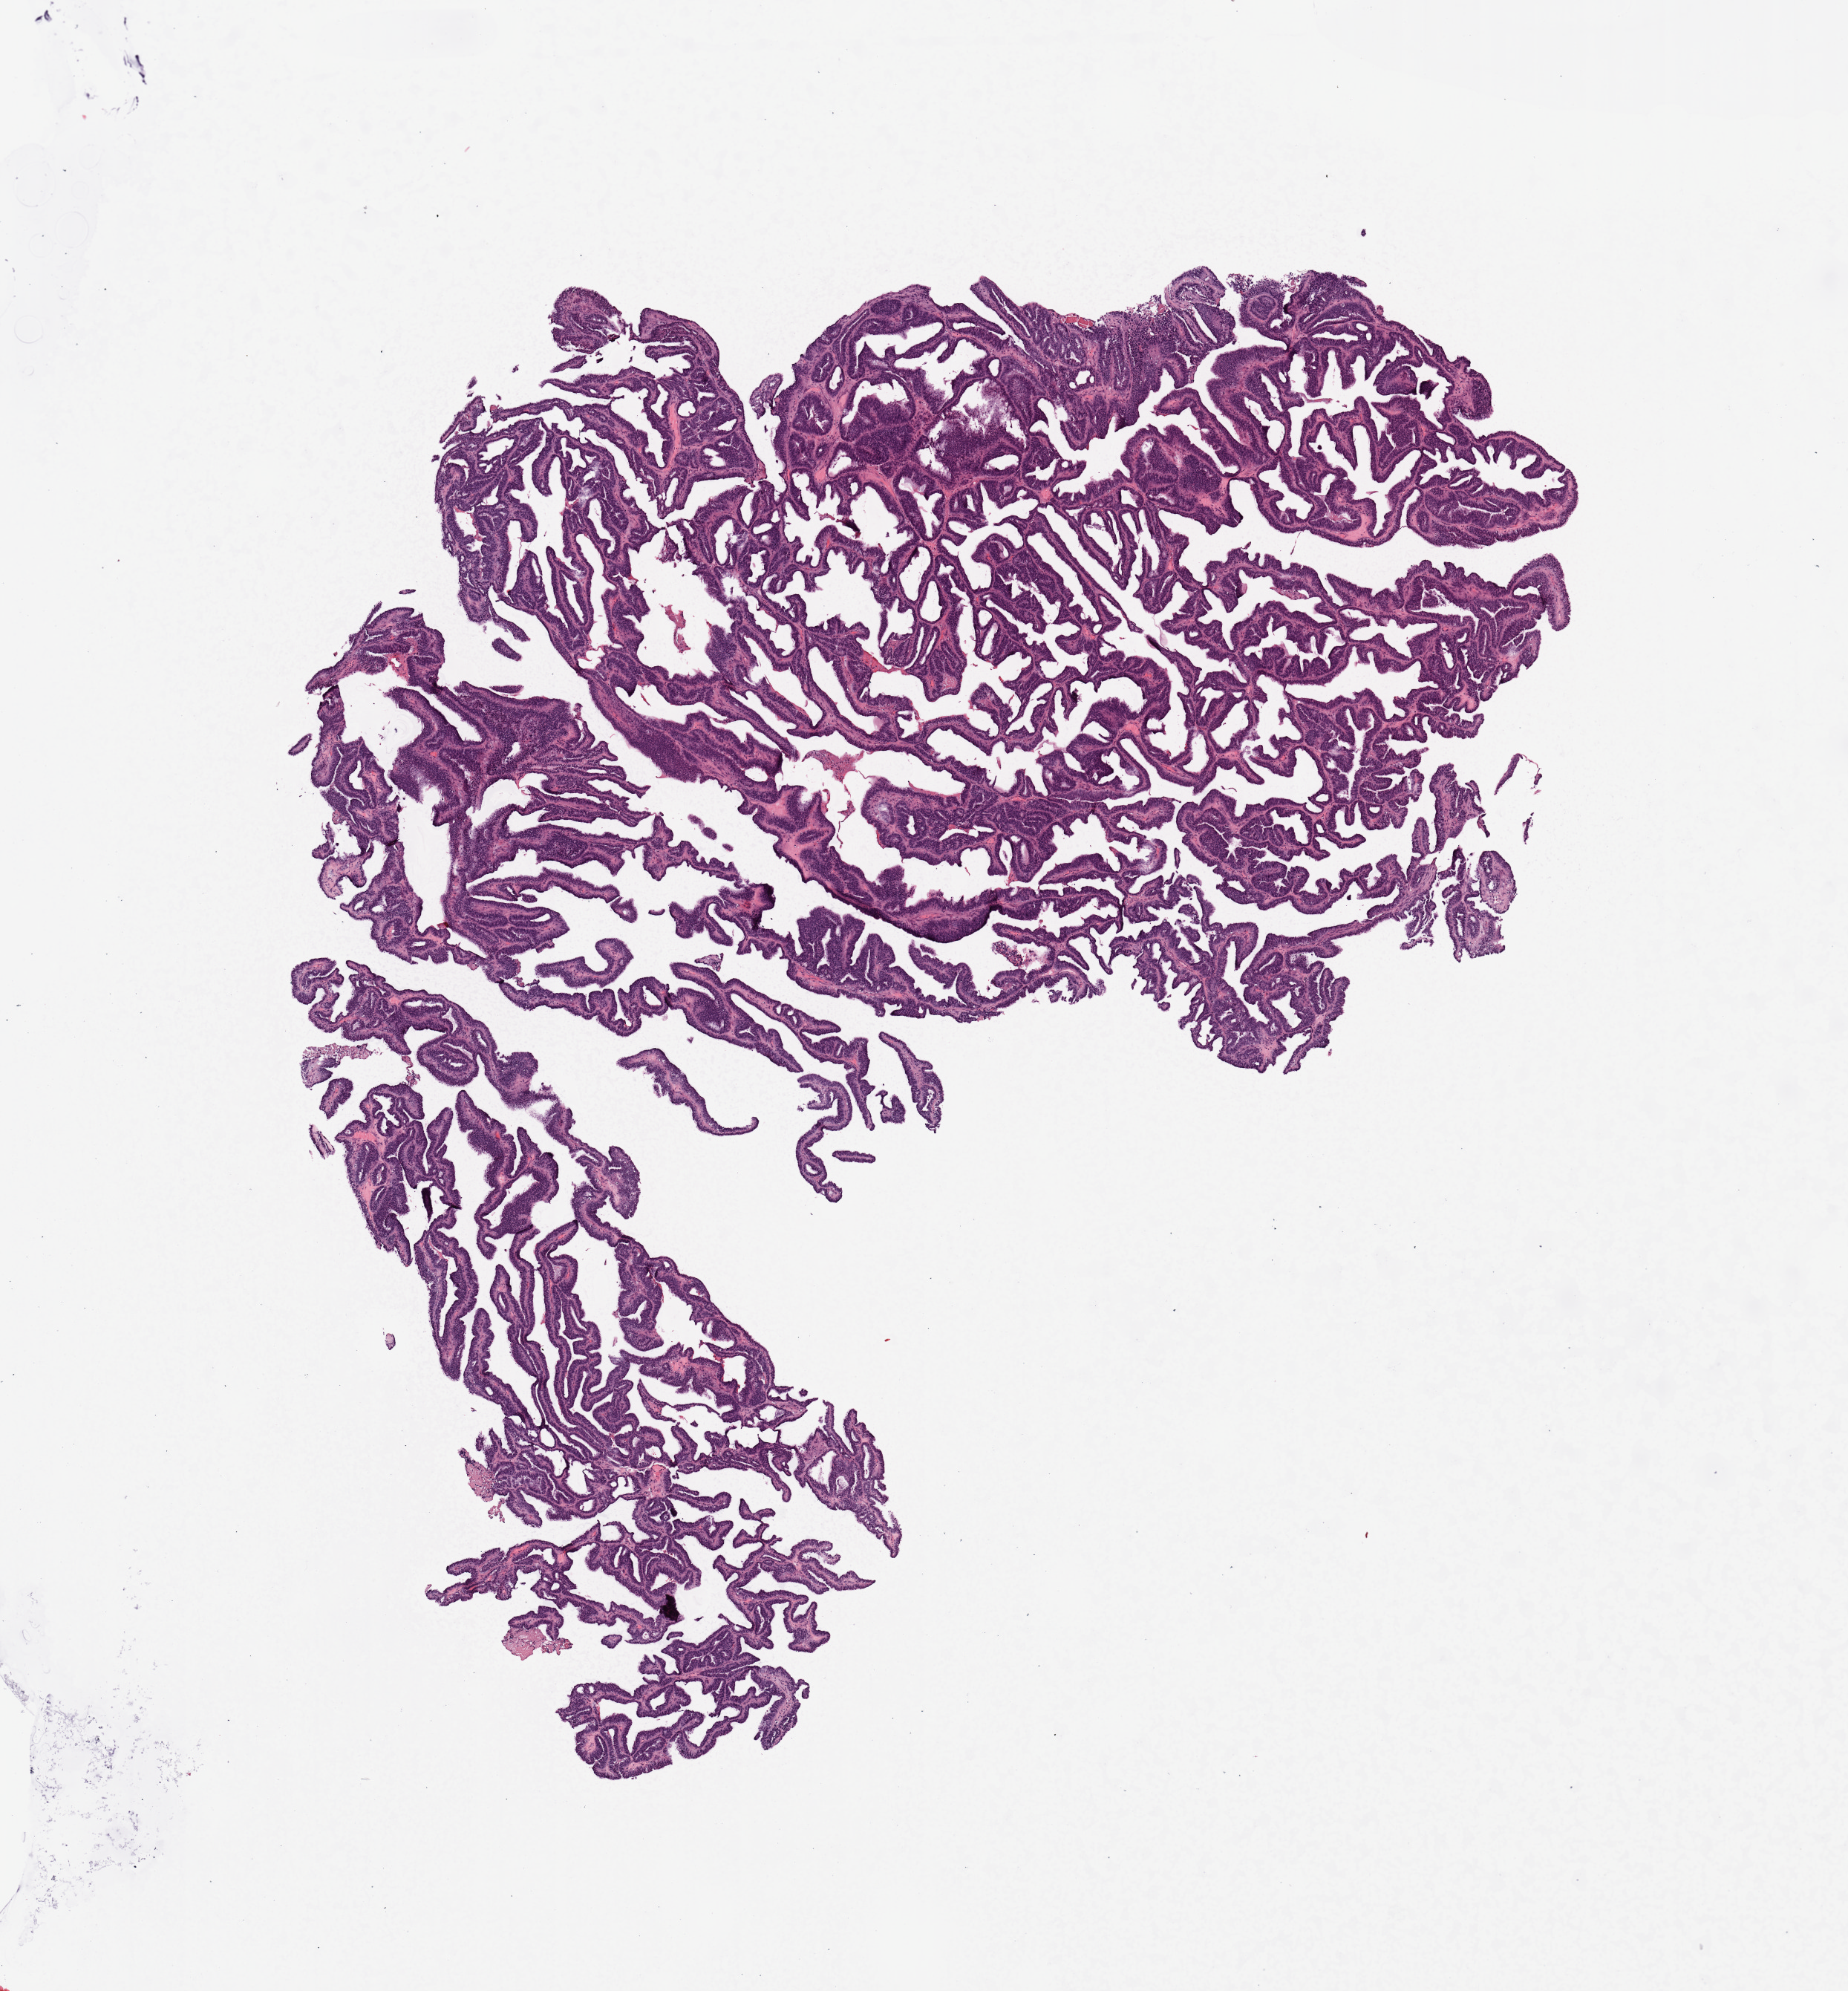
Whole-slide histology image, Hematoxylin and eosin (H&E) stained, whole scanned area (about 9.8 x 10.6 mm, from a 20x scan) shown as a low-resolution overview; tumour tissue sample, sampled site: uterus. Female, 53 y/o. Histologic grade: G2 (moderately differentiated). Composition of this section per pathologist review: tumour nuclei 90%, necrosis 0%.
AJCC pathologic stage: IIIA. Diagnosis: Endometrioid adenocarcinoma, NOS.